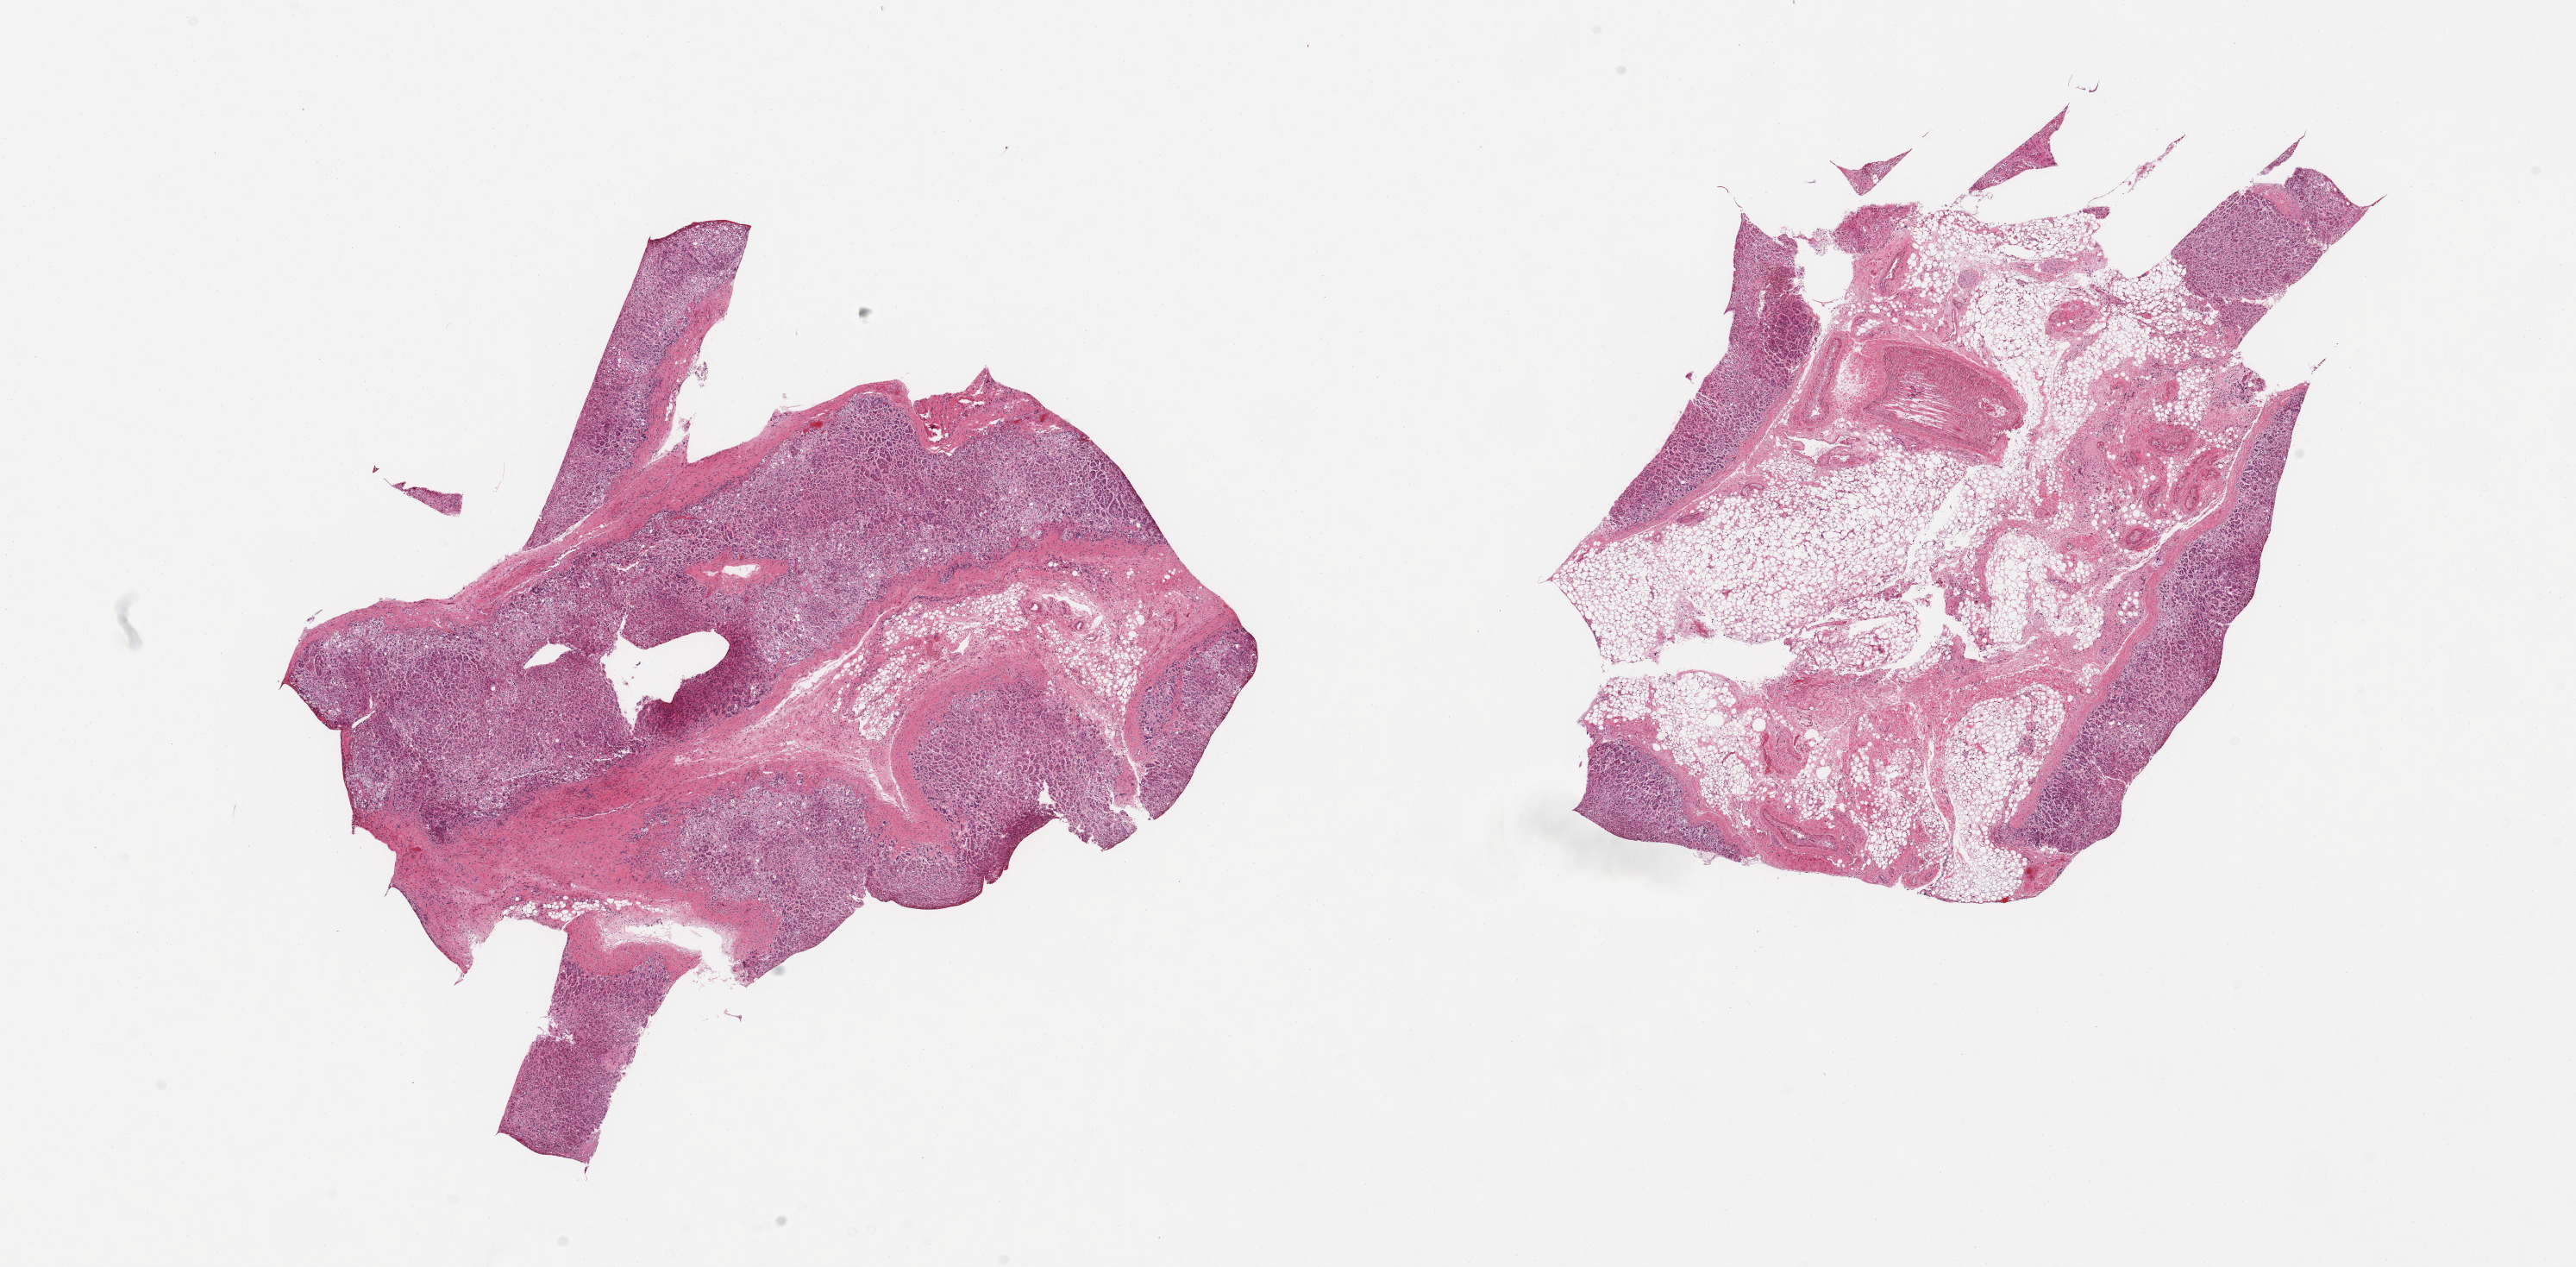
Digitized hematoxylin and eosin (H&E)-stained section, low-resolution overview of the scanned area, about 23.6 x 11.6 mm (from a 20x scan). PAXgene-fixed paraffin-embedded (PFPE) section. Section of adrenal gland (target tissue). Tissue donor sample. Female donor.
Reviewer comment on this tissue sample: 2 pieces, ~cortex, ~40% adherent/interstitial fat.